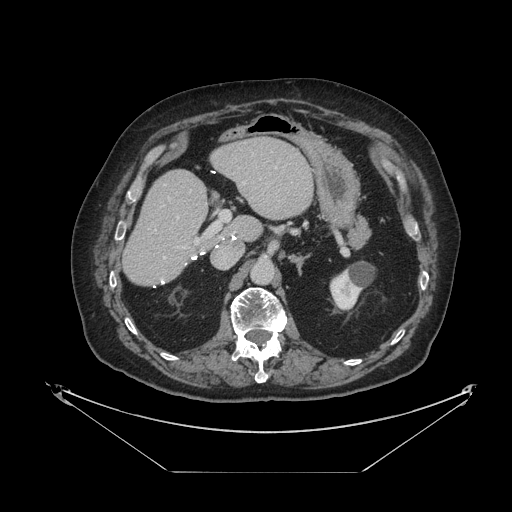
Contrast-enhanced abdominal CT, one axial slice; slice 56 of 121 in the series (ordered by position); reconstruction kernel STANDARD; 120 kVp; intravenous contrast given; soft-tissue window (W 400 / L 40 HU); 2.5 mm slice thickness; 512 × 512 image matrix. Male patient, age 68 years. Case-level facts recorded for this patient, not image findings: diagnosis: colorectal cancer liver metastases, imaged before liver resection; multiple liver metastases: no; largest metastasis: 4 cm; disease in both lobes: no.
Structures marked on this image (expert manual segmentation):
- hepatic veins: bounding box <164,167,277,259> (left, top, right, bottom; pixels)
- liver: <124,138,313,285>
- planned liver remnant (the part of the liver to remain after resection): <124,138,313,285>
- portal vein (with intrahepatic branches): <168,197,230,249>